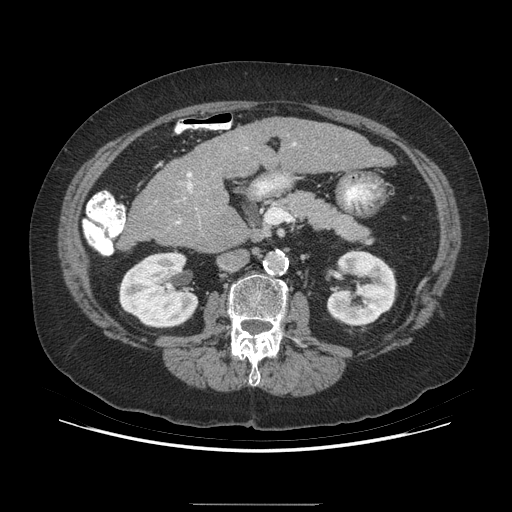
Contrast-enhanced abdominal CT (liver protocol), one axial slice. Position 139 of 192 along the scan axis. Reconstruction kernel STANDARD. 140 kVp. Soft-tissue window (W 400 / L 40 HU). 512 × 512 image matrix, field of view 400 × 400 mm. From the clinical record (not read from this slice): diagnosis: hepatocellular carcinoma (patient treated with transarterial chemoembolisation; whether this scan precedes or follows treatment is not stated here); TNM stage (as recorded): Stage-I; Child-Pugh class: A; tumour differentiation: moderately differentiated; tumour nodularity: uninodular.
Outlined on this slice (semi-automatically segmented with operator editing):
- liver parenchyma outside the tumour (the mass and vessels are separate outlines, so this box may not span the whole liver): bounding box <123,118,394,252> (left, top, right, bottom; pixels)
- liver vessels: <176,143,296,224>